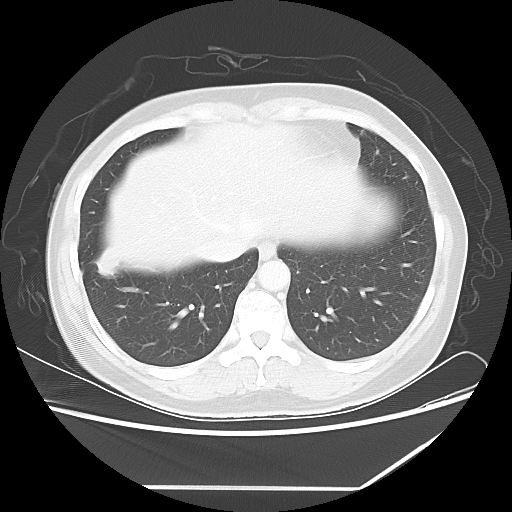
Chest CT, one axial slice. Slice 18 of 60 in the series (ordered by position). Reconstruction kernel LUNG. 100 kVp. Lung window (W 1500 / L -600 HU). 5 mm slice thickness. 512 × 512 image matrix, field of view 374 × 374 mm. Female patient, age 42 years. Case-level facts recorded for this patient, not image findings: clinical TNM (as recorded): T2 N1 M0.
Structures marked on this image (bounding box drawn by a radiologist):
- lung tumour (recorded histology: adenocarcinoma): bounding box <92,245,122,283> (left, top, right, bottom; pixels)